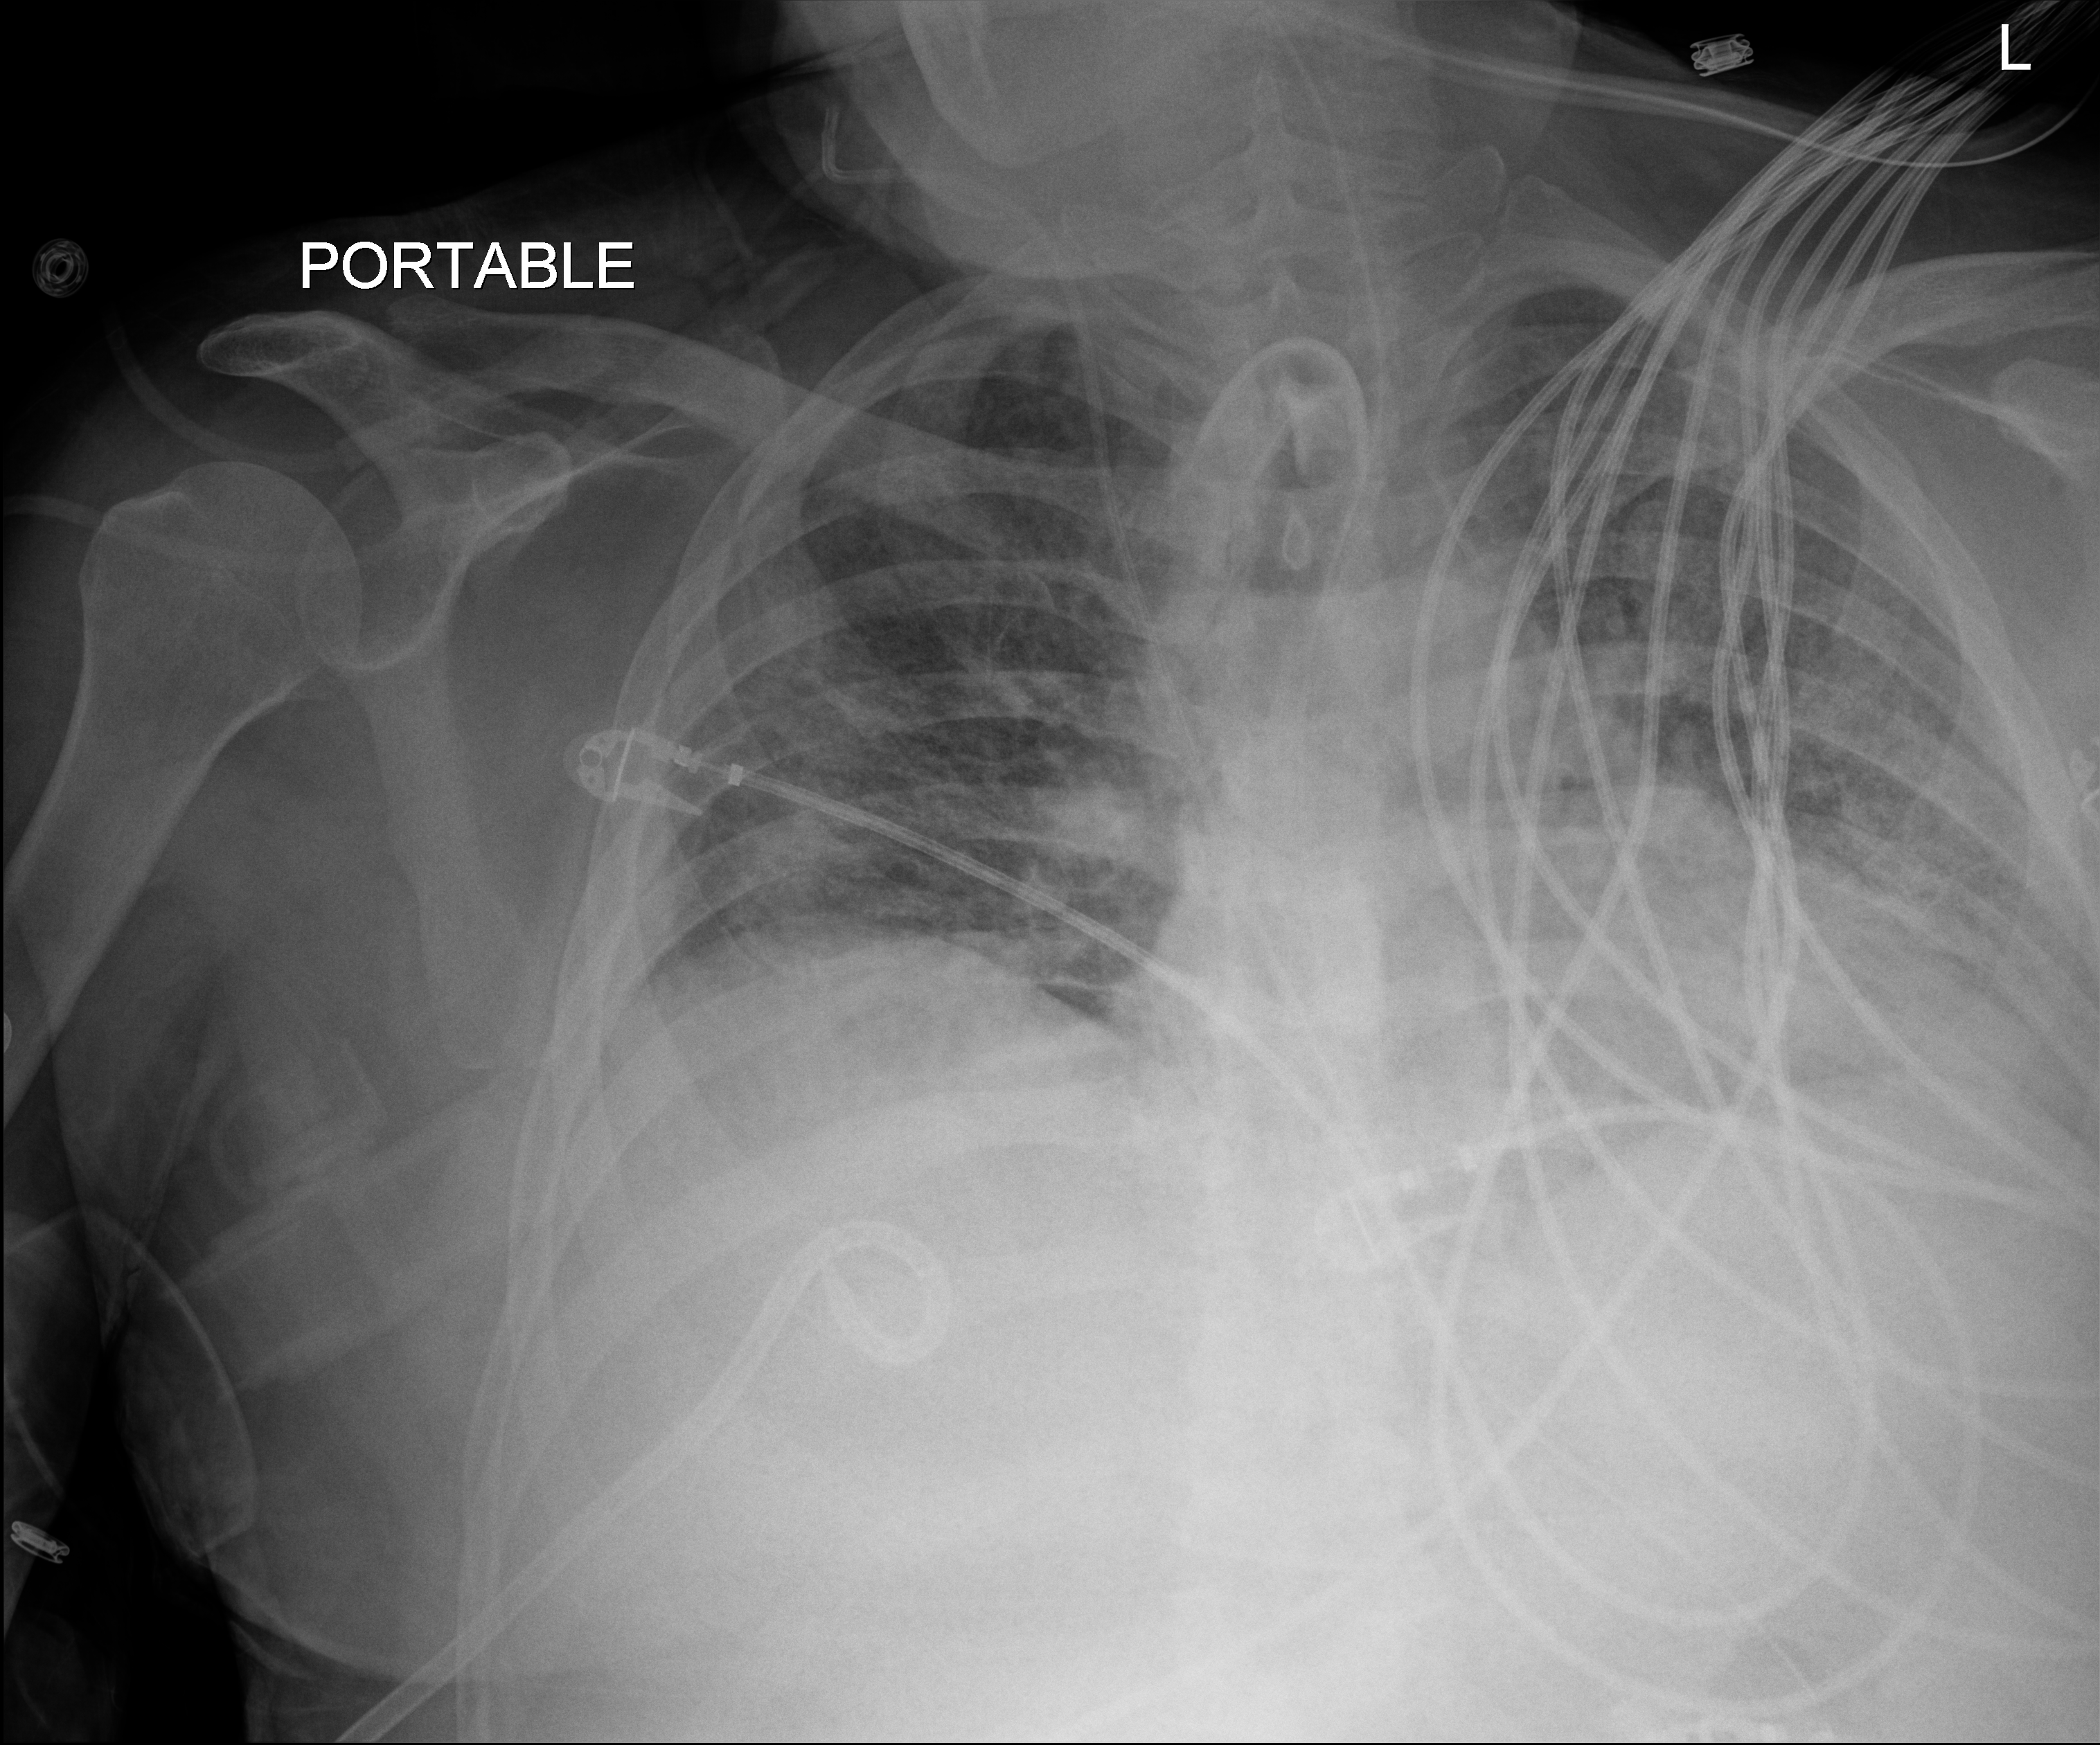
Bedside chest radiograph (digital radiography); anteroposterior (AP) projection. Patient hospitalised with COVID-19; male, aged 18–59 years.
From the hospital-stay record, not from the radiograph (when in the stay this image was taken is not recorded):
- admitted to intensive care during this hospital stay: yes
- length of hospital stay: 80 days
- mechanically ventilated during this hospital stay: yes